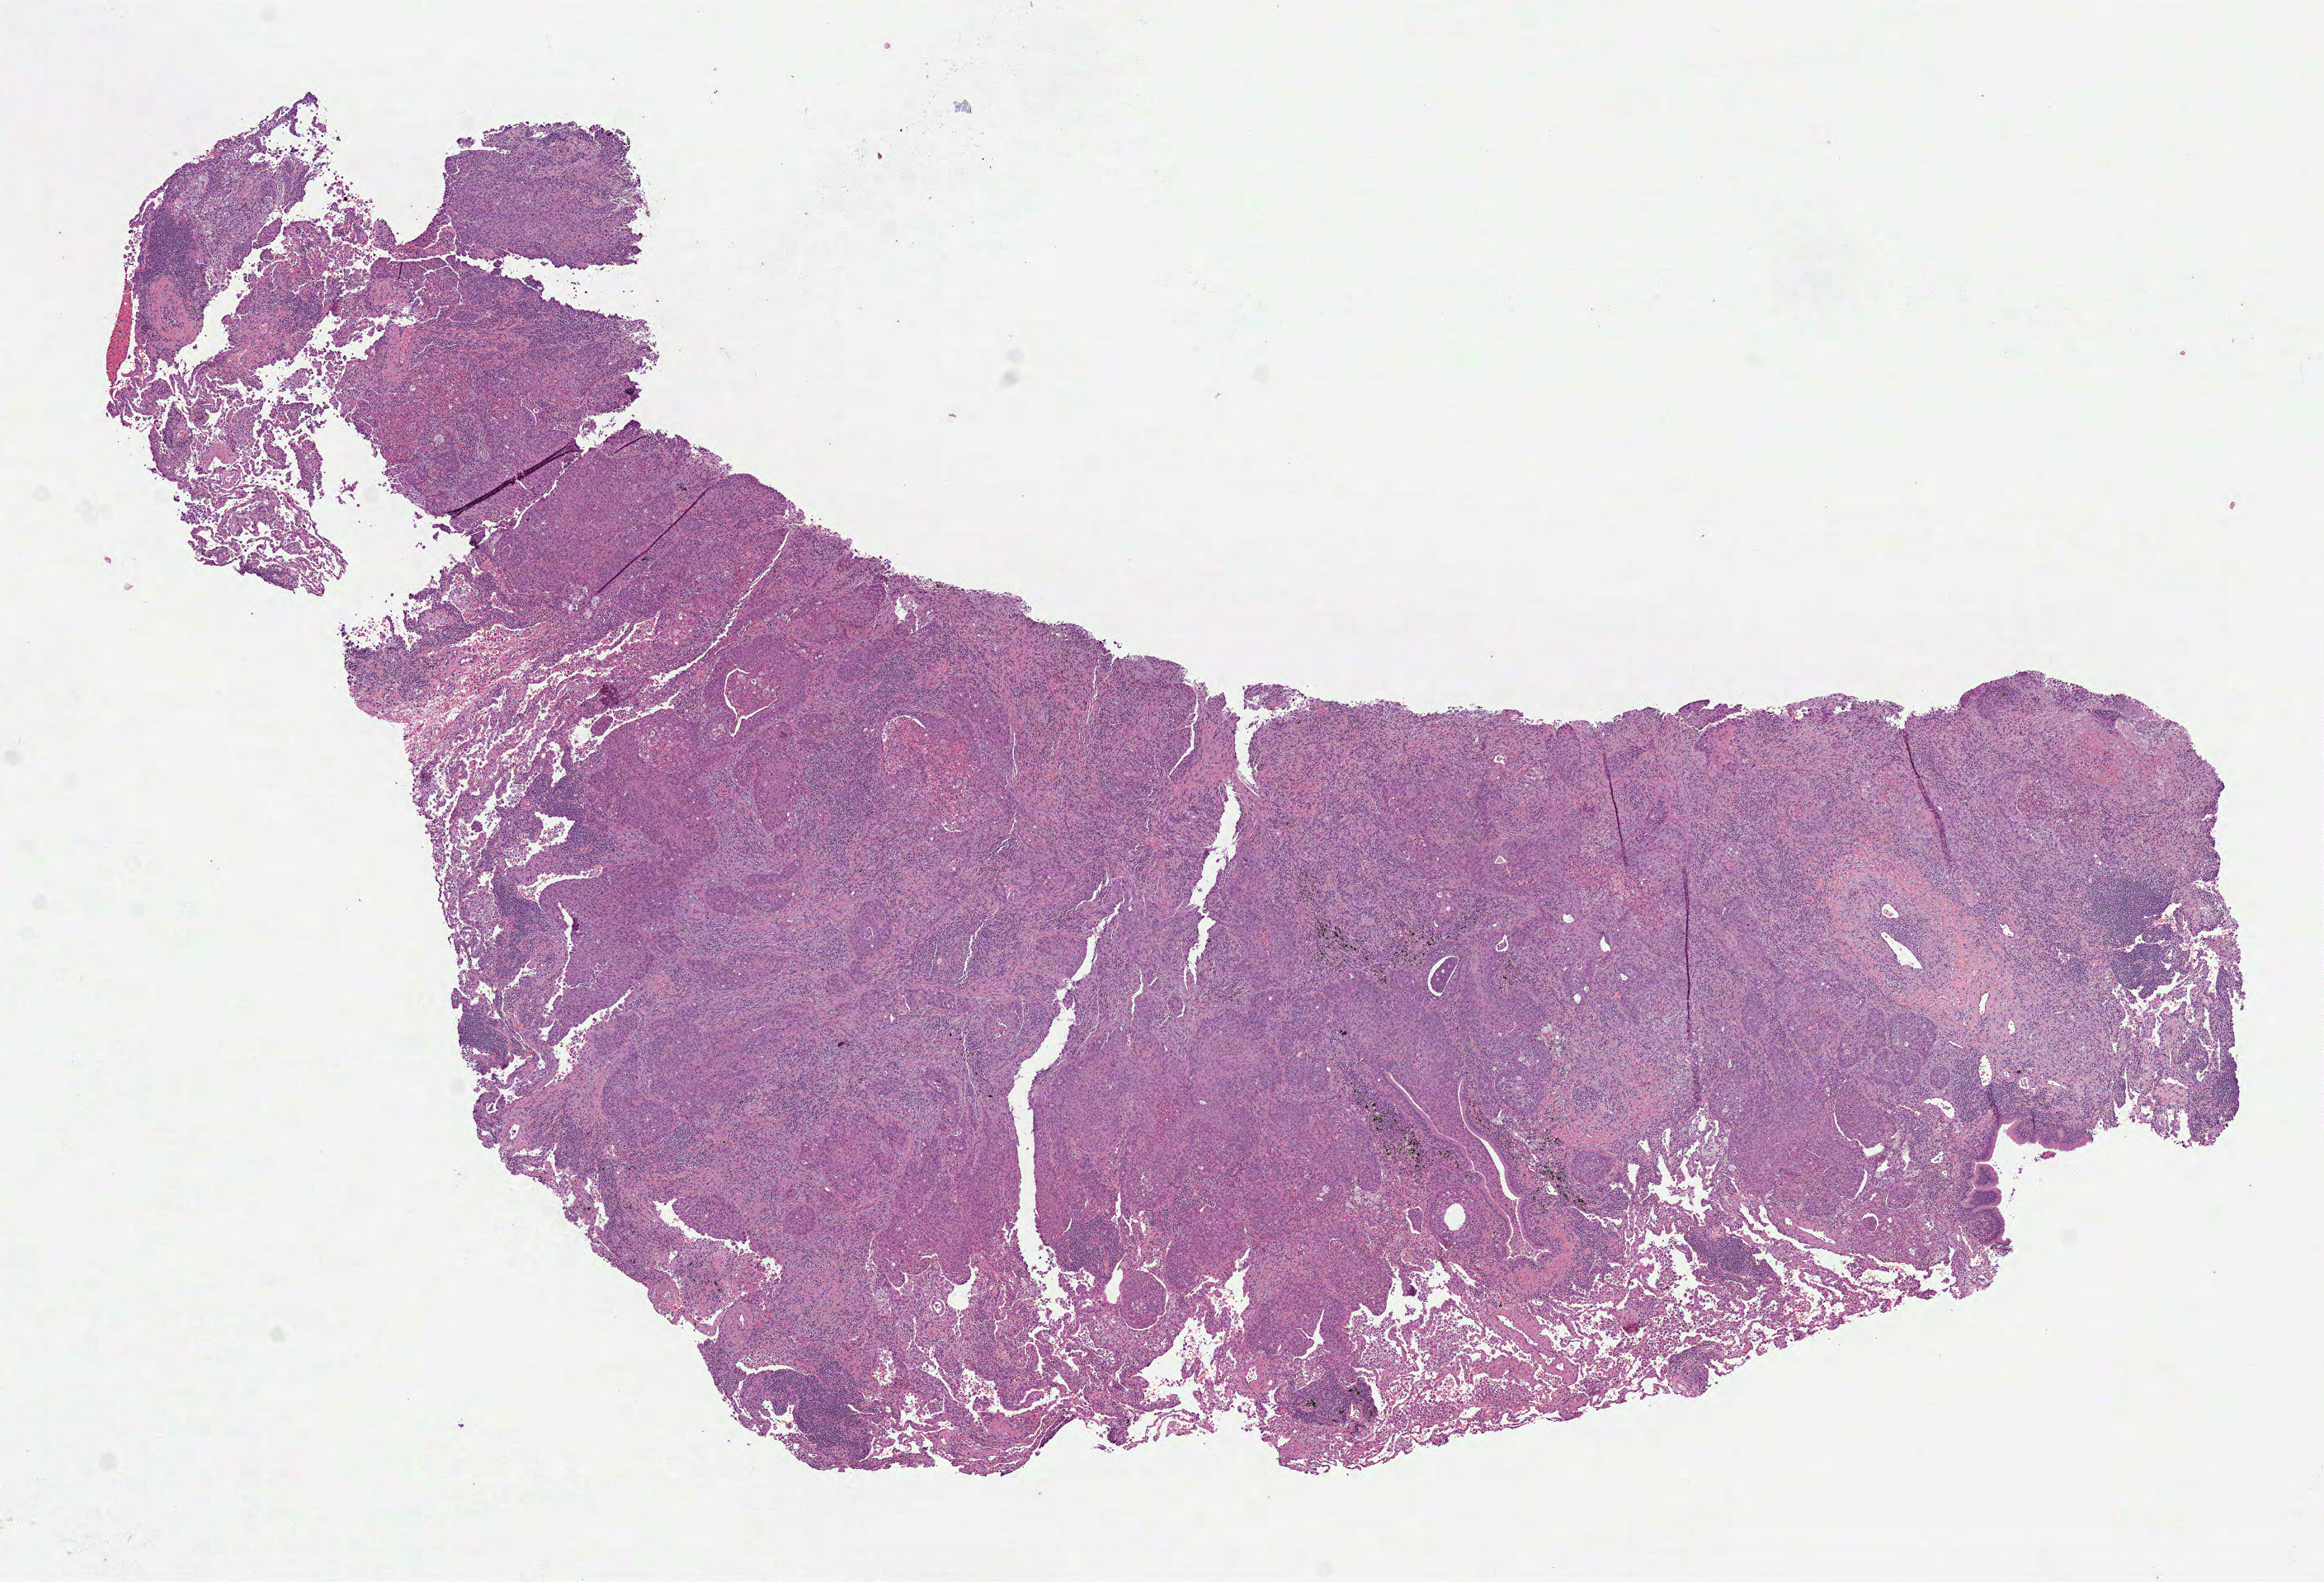
H&E-stained whole-slide image — shown as a low-resolution overview of the whole scanned area (about 11.4 x 7.7 mm); formalin-fixed paraffin-embedded (FFPE) diagnostic section; primary tumour sample from the lung. Male, age 74 years at initial diagnosis.
AJCC pathologic stage: IA. Histologic diagnosis: Squamous cell carcinoma, NOS (upper lobe, lung). TNM: T1b N0 MX. Laterality: right.